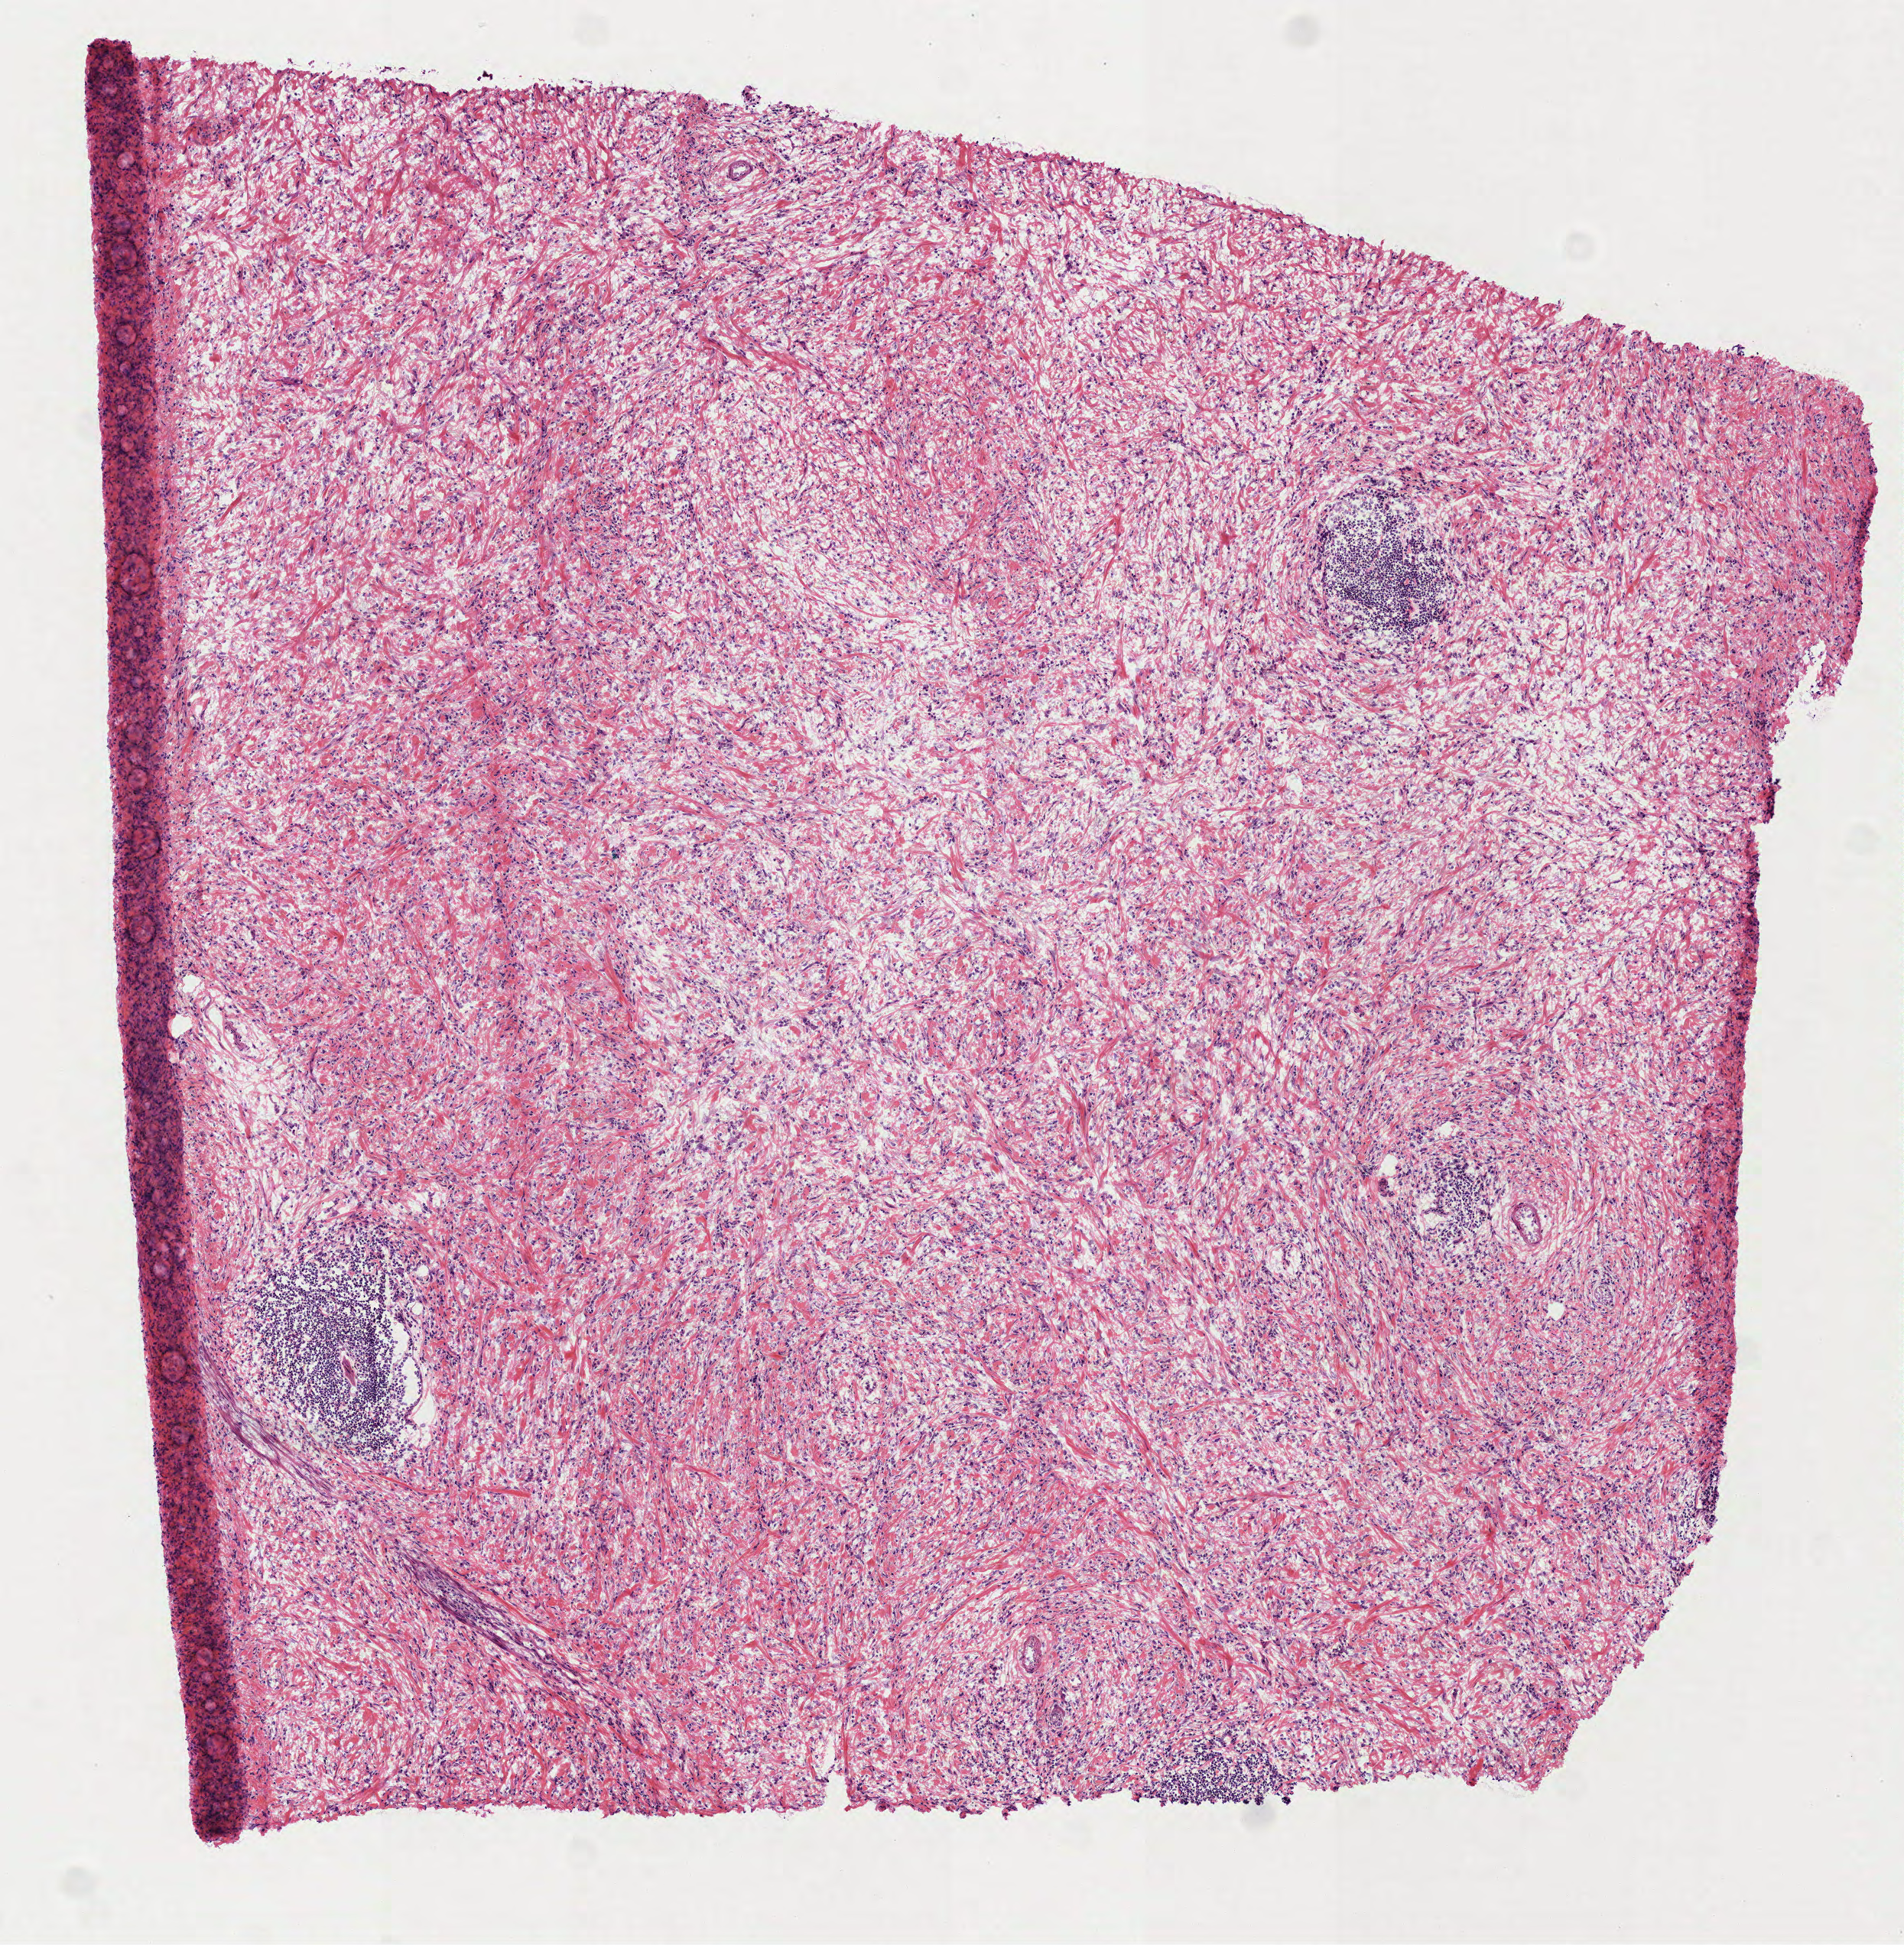
Digitized H&E tissue section (whole slide) — low-resolution overview of the scanned area, about 5.0 x 5.1 mm. Frozen section from the top of the tissue portion. Stomach, primary tumour sample. Male, age 72 years at initial diagnosis. Histologic grade: G3 (poorly differentiated). Slide review estimates, as recorded: tumour cells 70%, tumour nuclei 65%, normal cells 0%, stromal cells 30%, necrosis 0%. Infiltration values recorded for this section: lymphocyte infiltration 20%, monocyte infiltration 0%, neutrophil infiltration 0%.
• TNM: T2 N3a M0
• AJCC pathologic stage: IIIA (7th edition)
• pathologic diagnosis: Adenocarcinoma, NOS (gastric antrum)